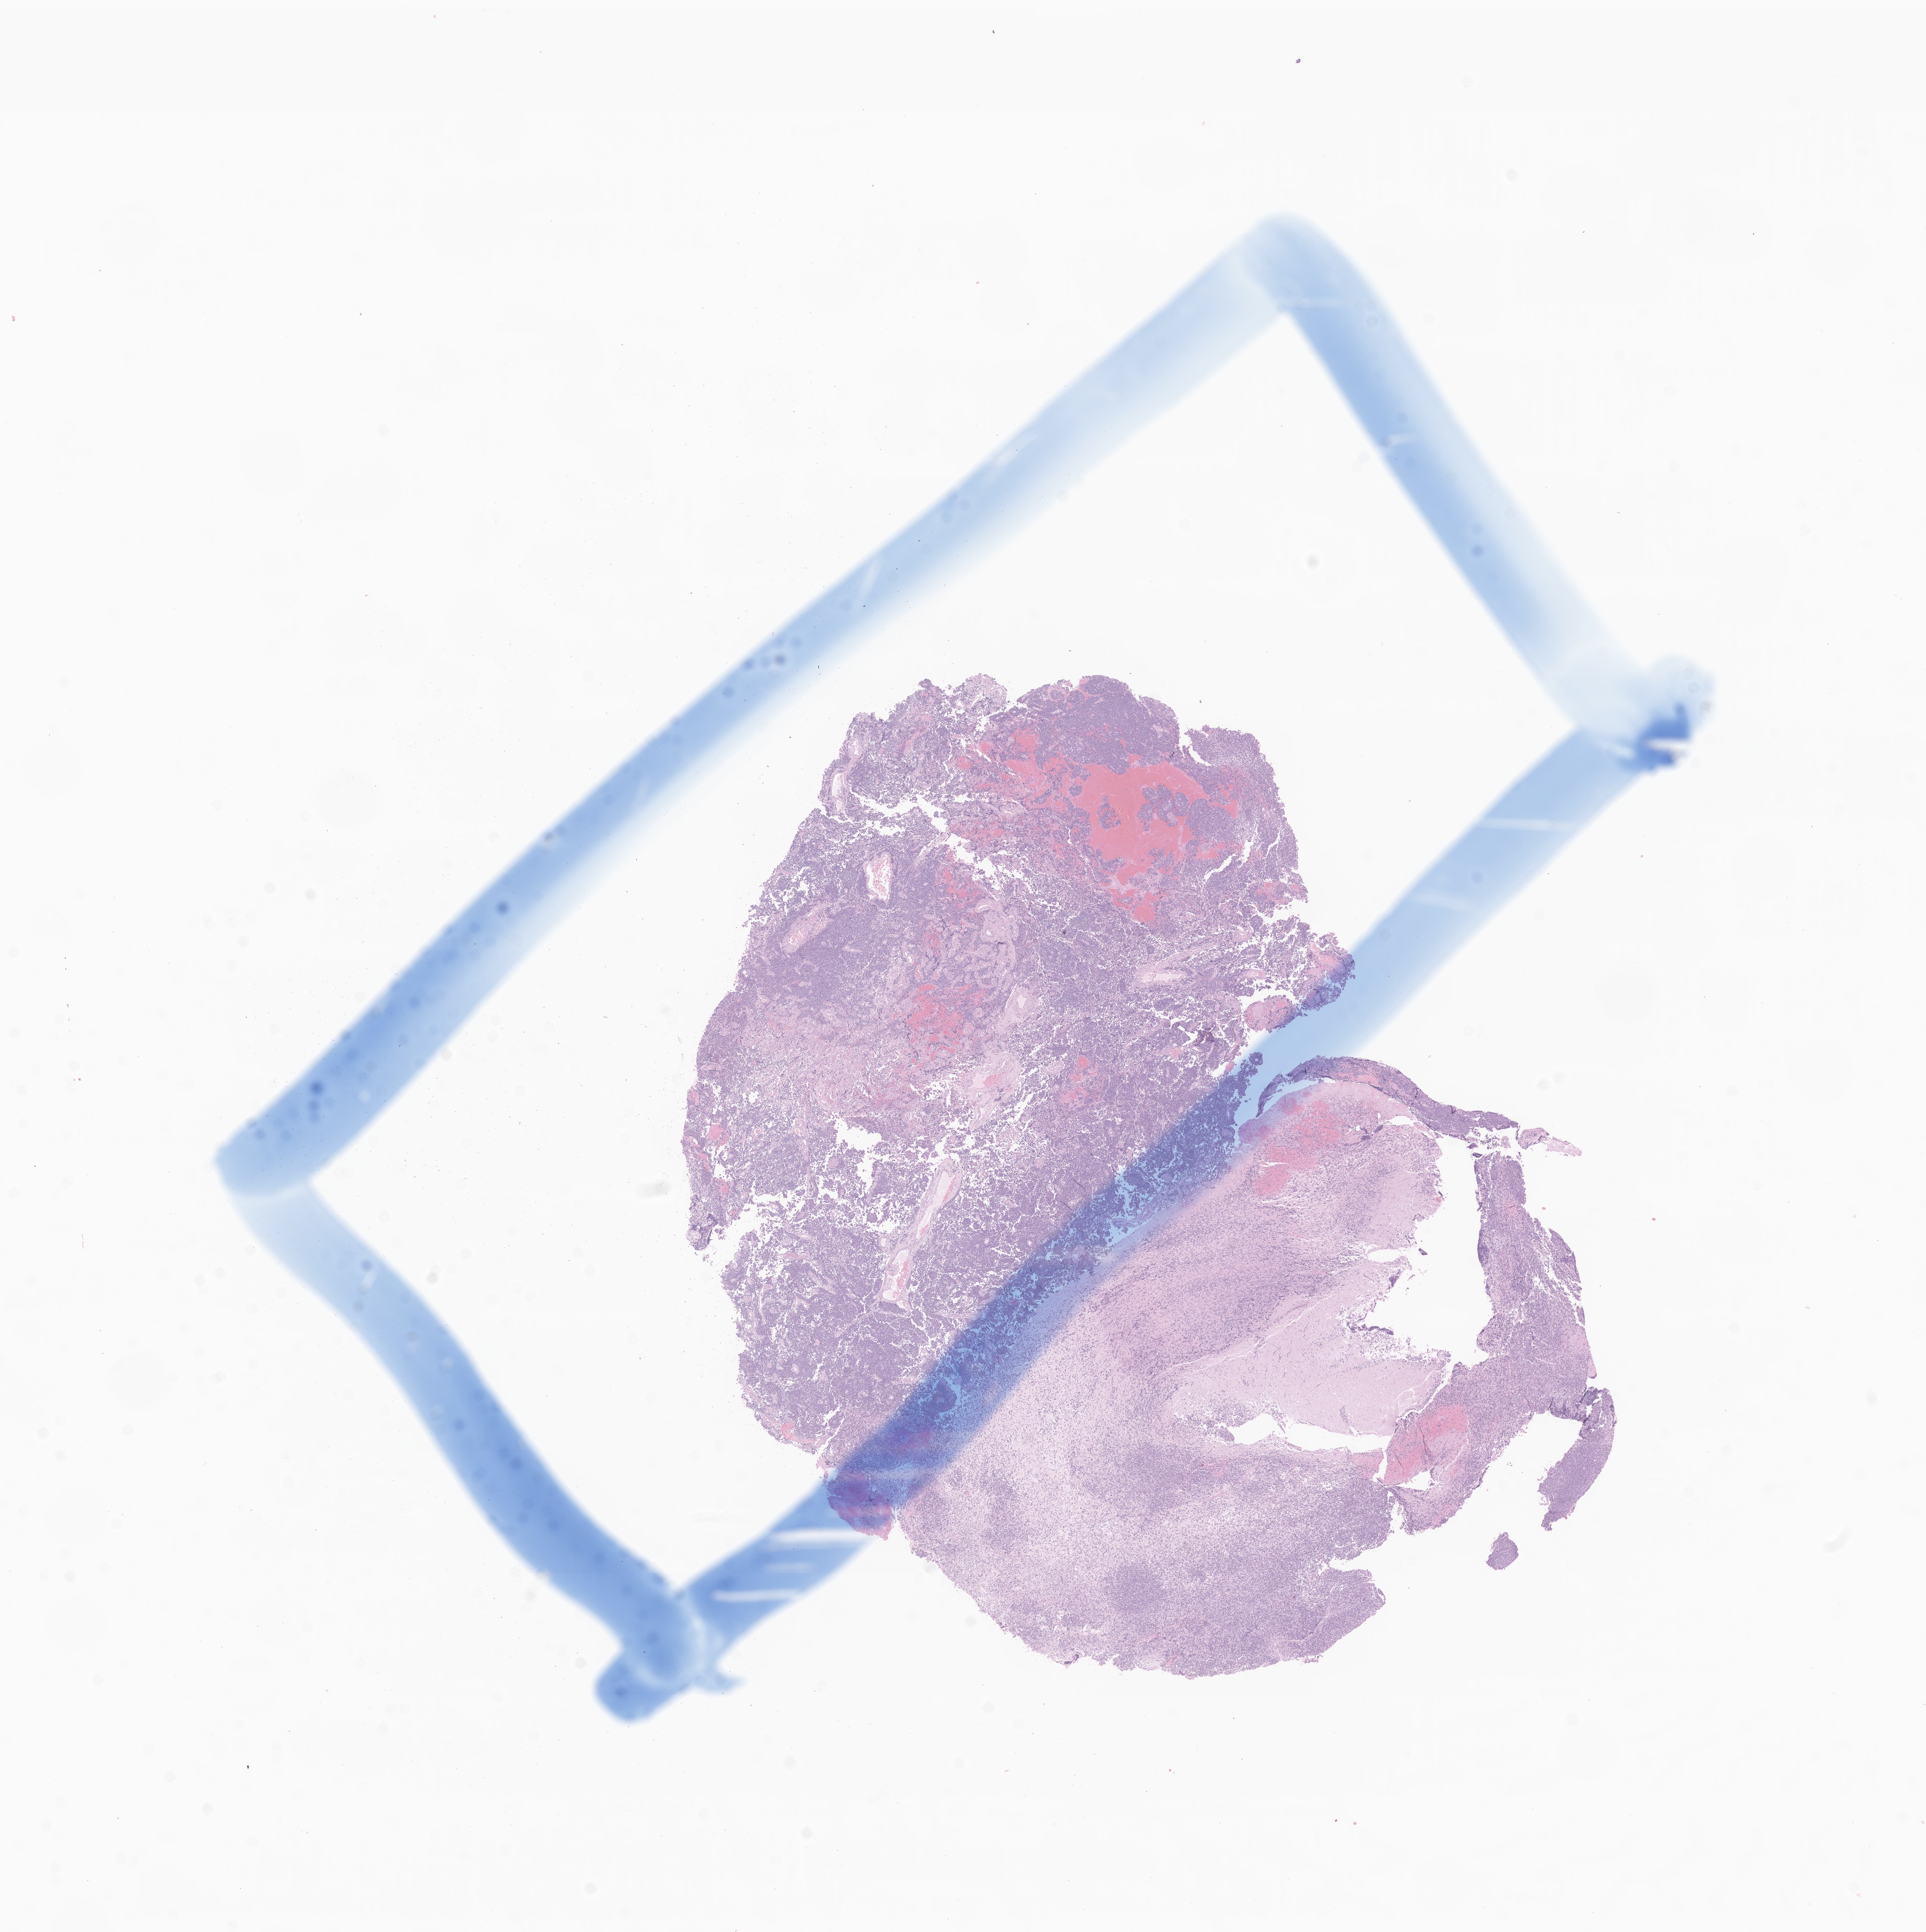
Hematoxylin and eosin (H&E) whole-slide image of tumor tissue from the brain, low-resolution overview of the scanned area, about 16.9 x 16.9 mm. Formalin-fixed, paraffin-embedded (FFPE) tissue. Male patient, age 106 months (8 years 10 months).
Diagnosis: Medulloblastoma, NOS.